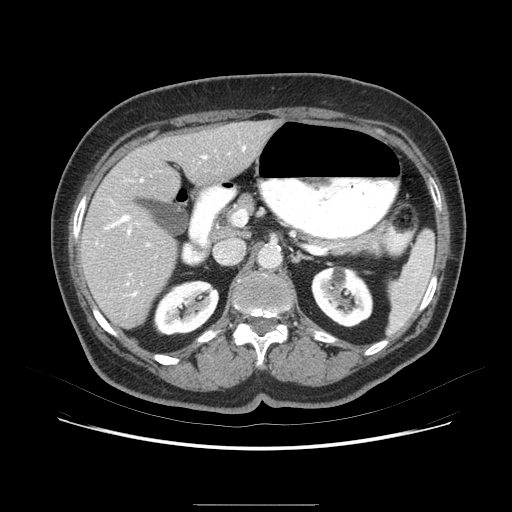
Contrast-enhanced abdominal CT (liver protocol), one axial slice; position 39 of 79 along the scan axis; 120 kVp; soft-tissue window (W 400 / L 40 HU); 2.5 mm slice thickness; 512 × 512 image matrix. Case-level facts recorded for this patient, not image findings: diagnosis: hepatocellular carcinoma (patient treated with transarterial chemoembolisation; whether this scan precedes or follows treatment is not stated here); TNM stage (as recorded): Stage-I; Child-Pugh class: A; tumour differentiation: poorly differentiated; tumour nodularity: uninodular.
Annotated regions visible in this slice (semi-automatically segmented with operator editing):
- liver parenchyma outside the tumour (the mass and vessels are separate outlines, so this box may not span the whole liver): bounding box (x1, y1, x2, y2) in pixels: (78, 120, 285, 336)
- mass: (123, 203, 168, 244)
- liver vessels: (113, 139, 259, 306)